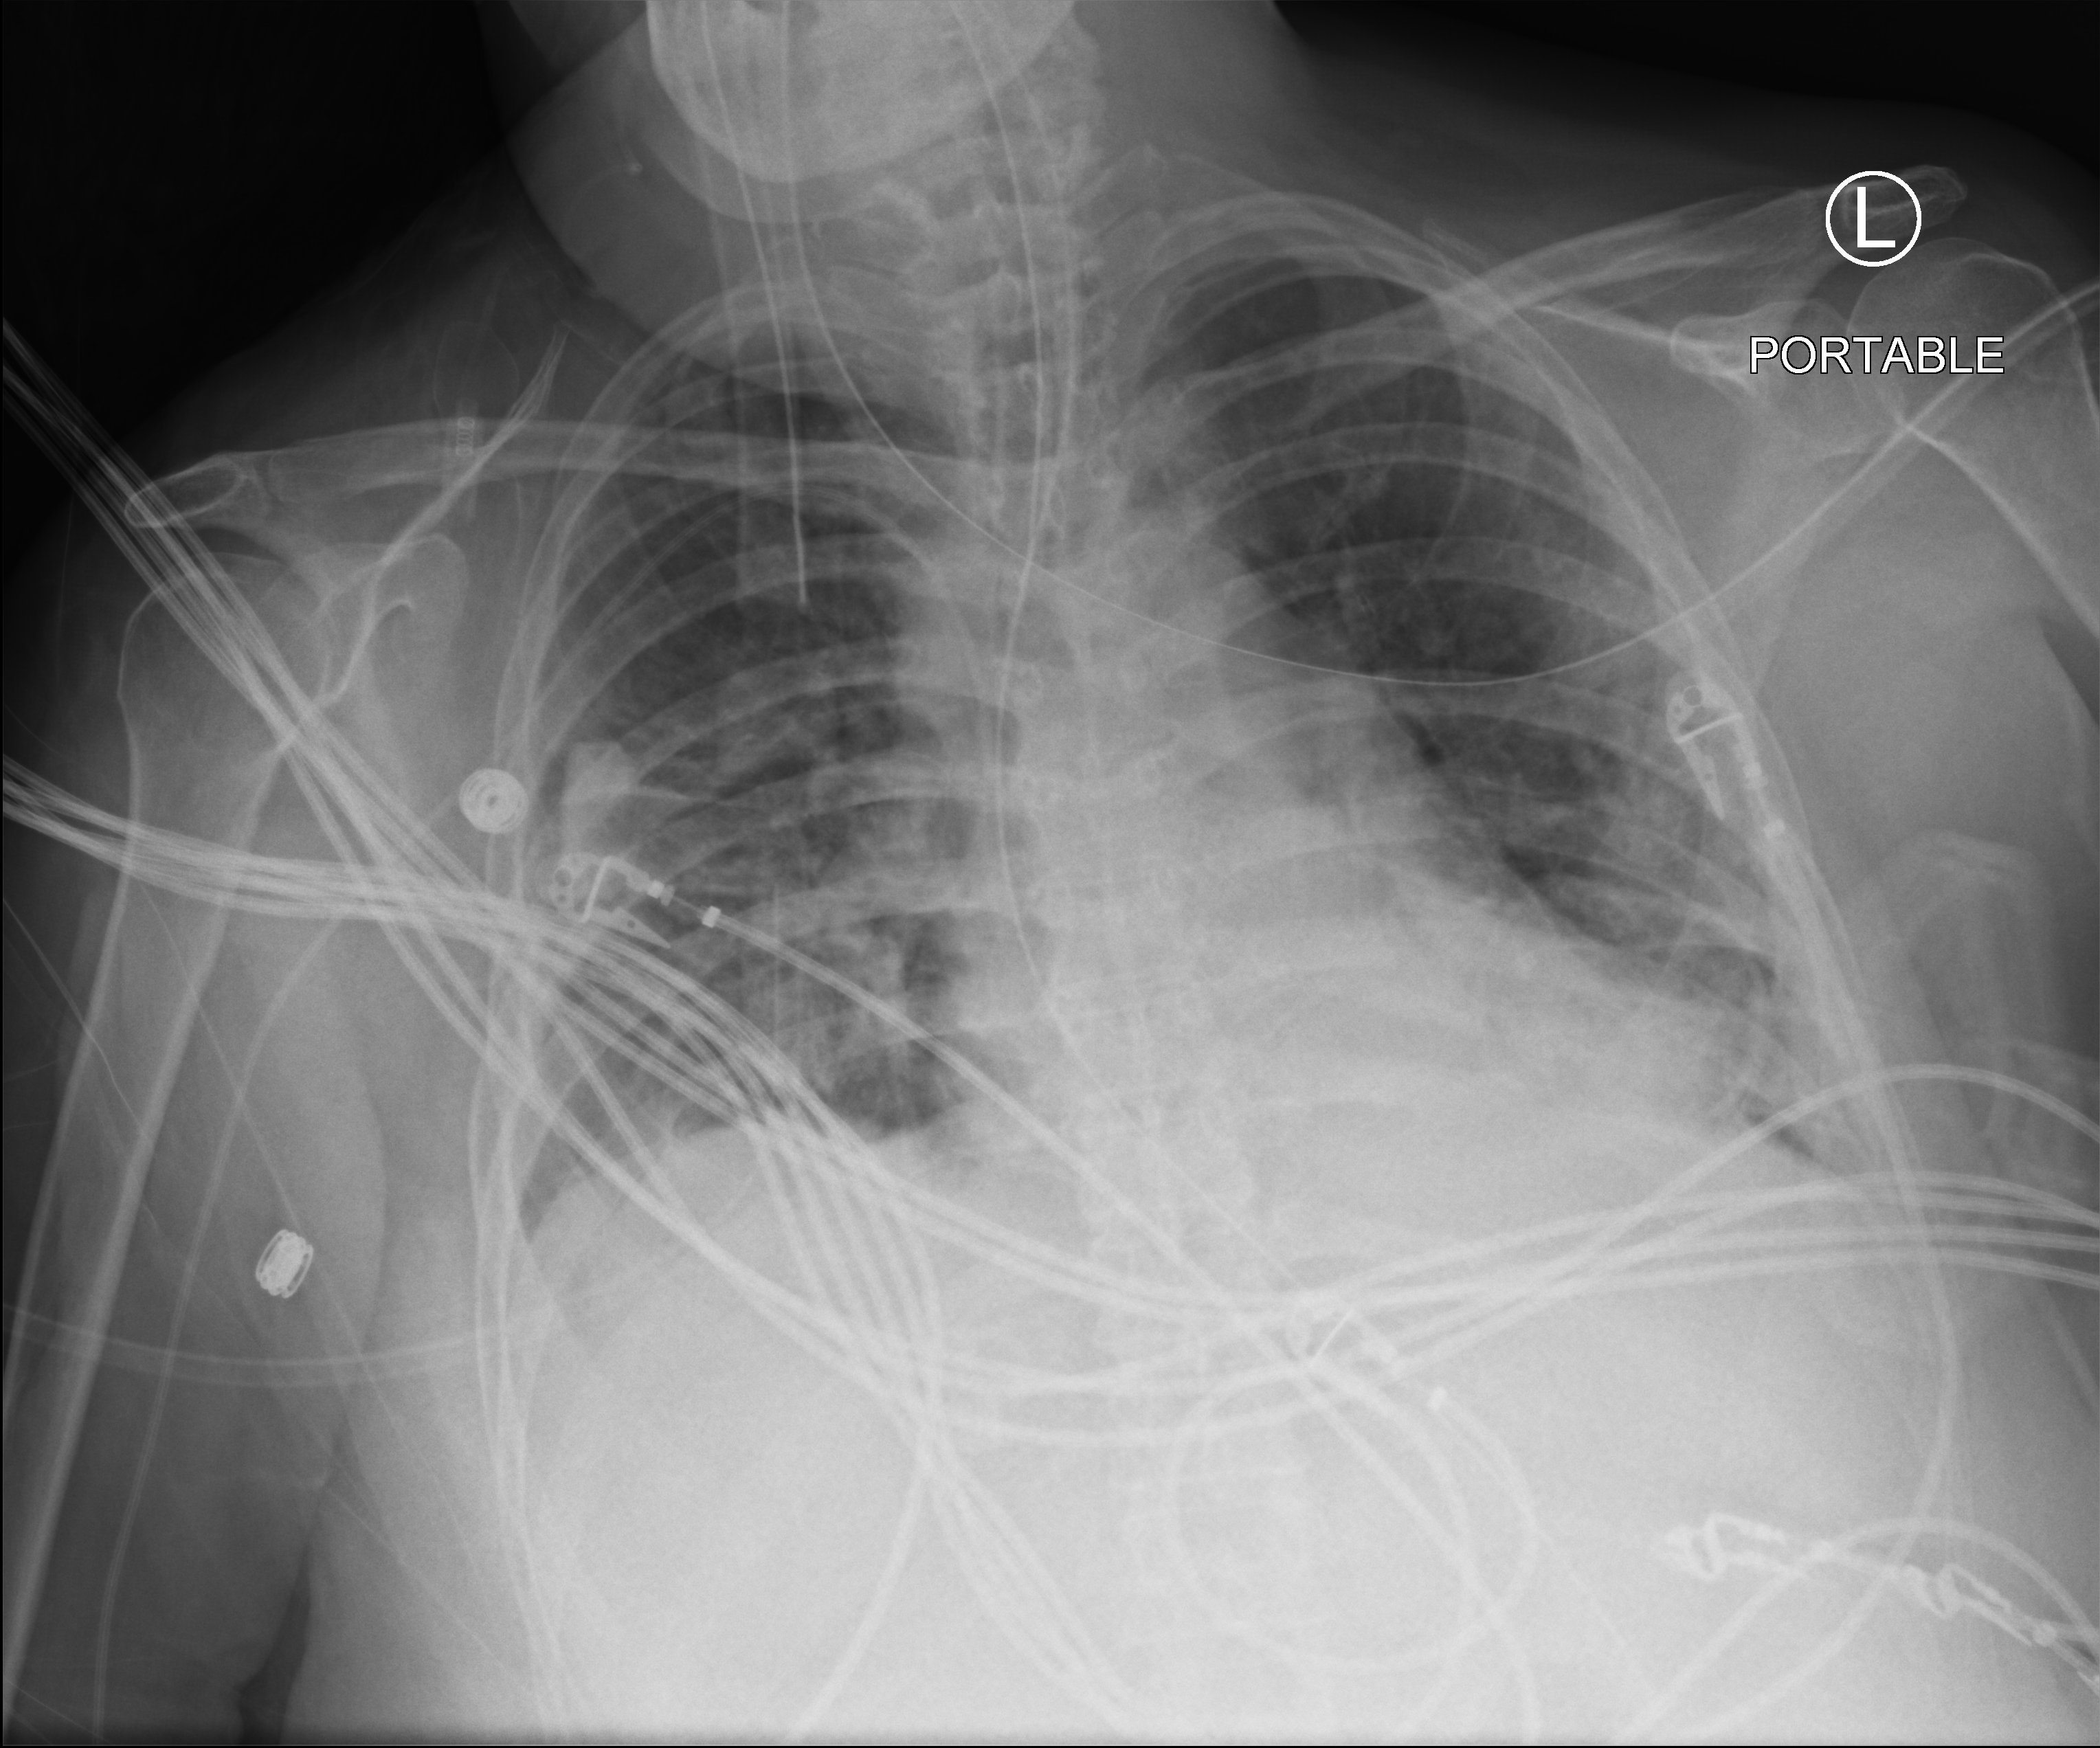
Bedside chest radiograph (computed radiography); anteroposterior (AP) projection. Female patient hospitalised with COVID-19, age 60–74 years.
Admission-level facts for this patient (not findings on this image; timing relative to this image not recorded):
- admitted to intensive care during this hospital stay: yes
- length of hospital stay: 9 days
- mechanically ventilated during this hospital stay: yes